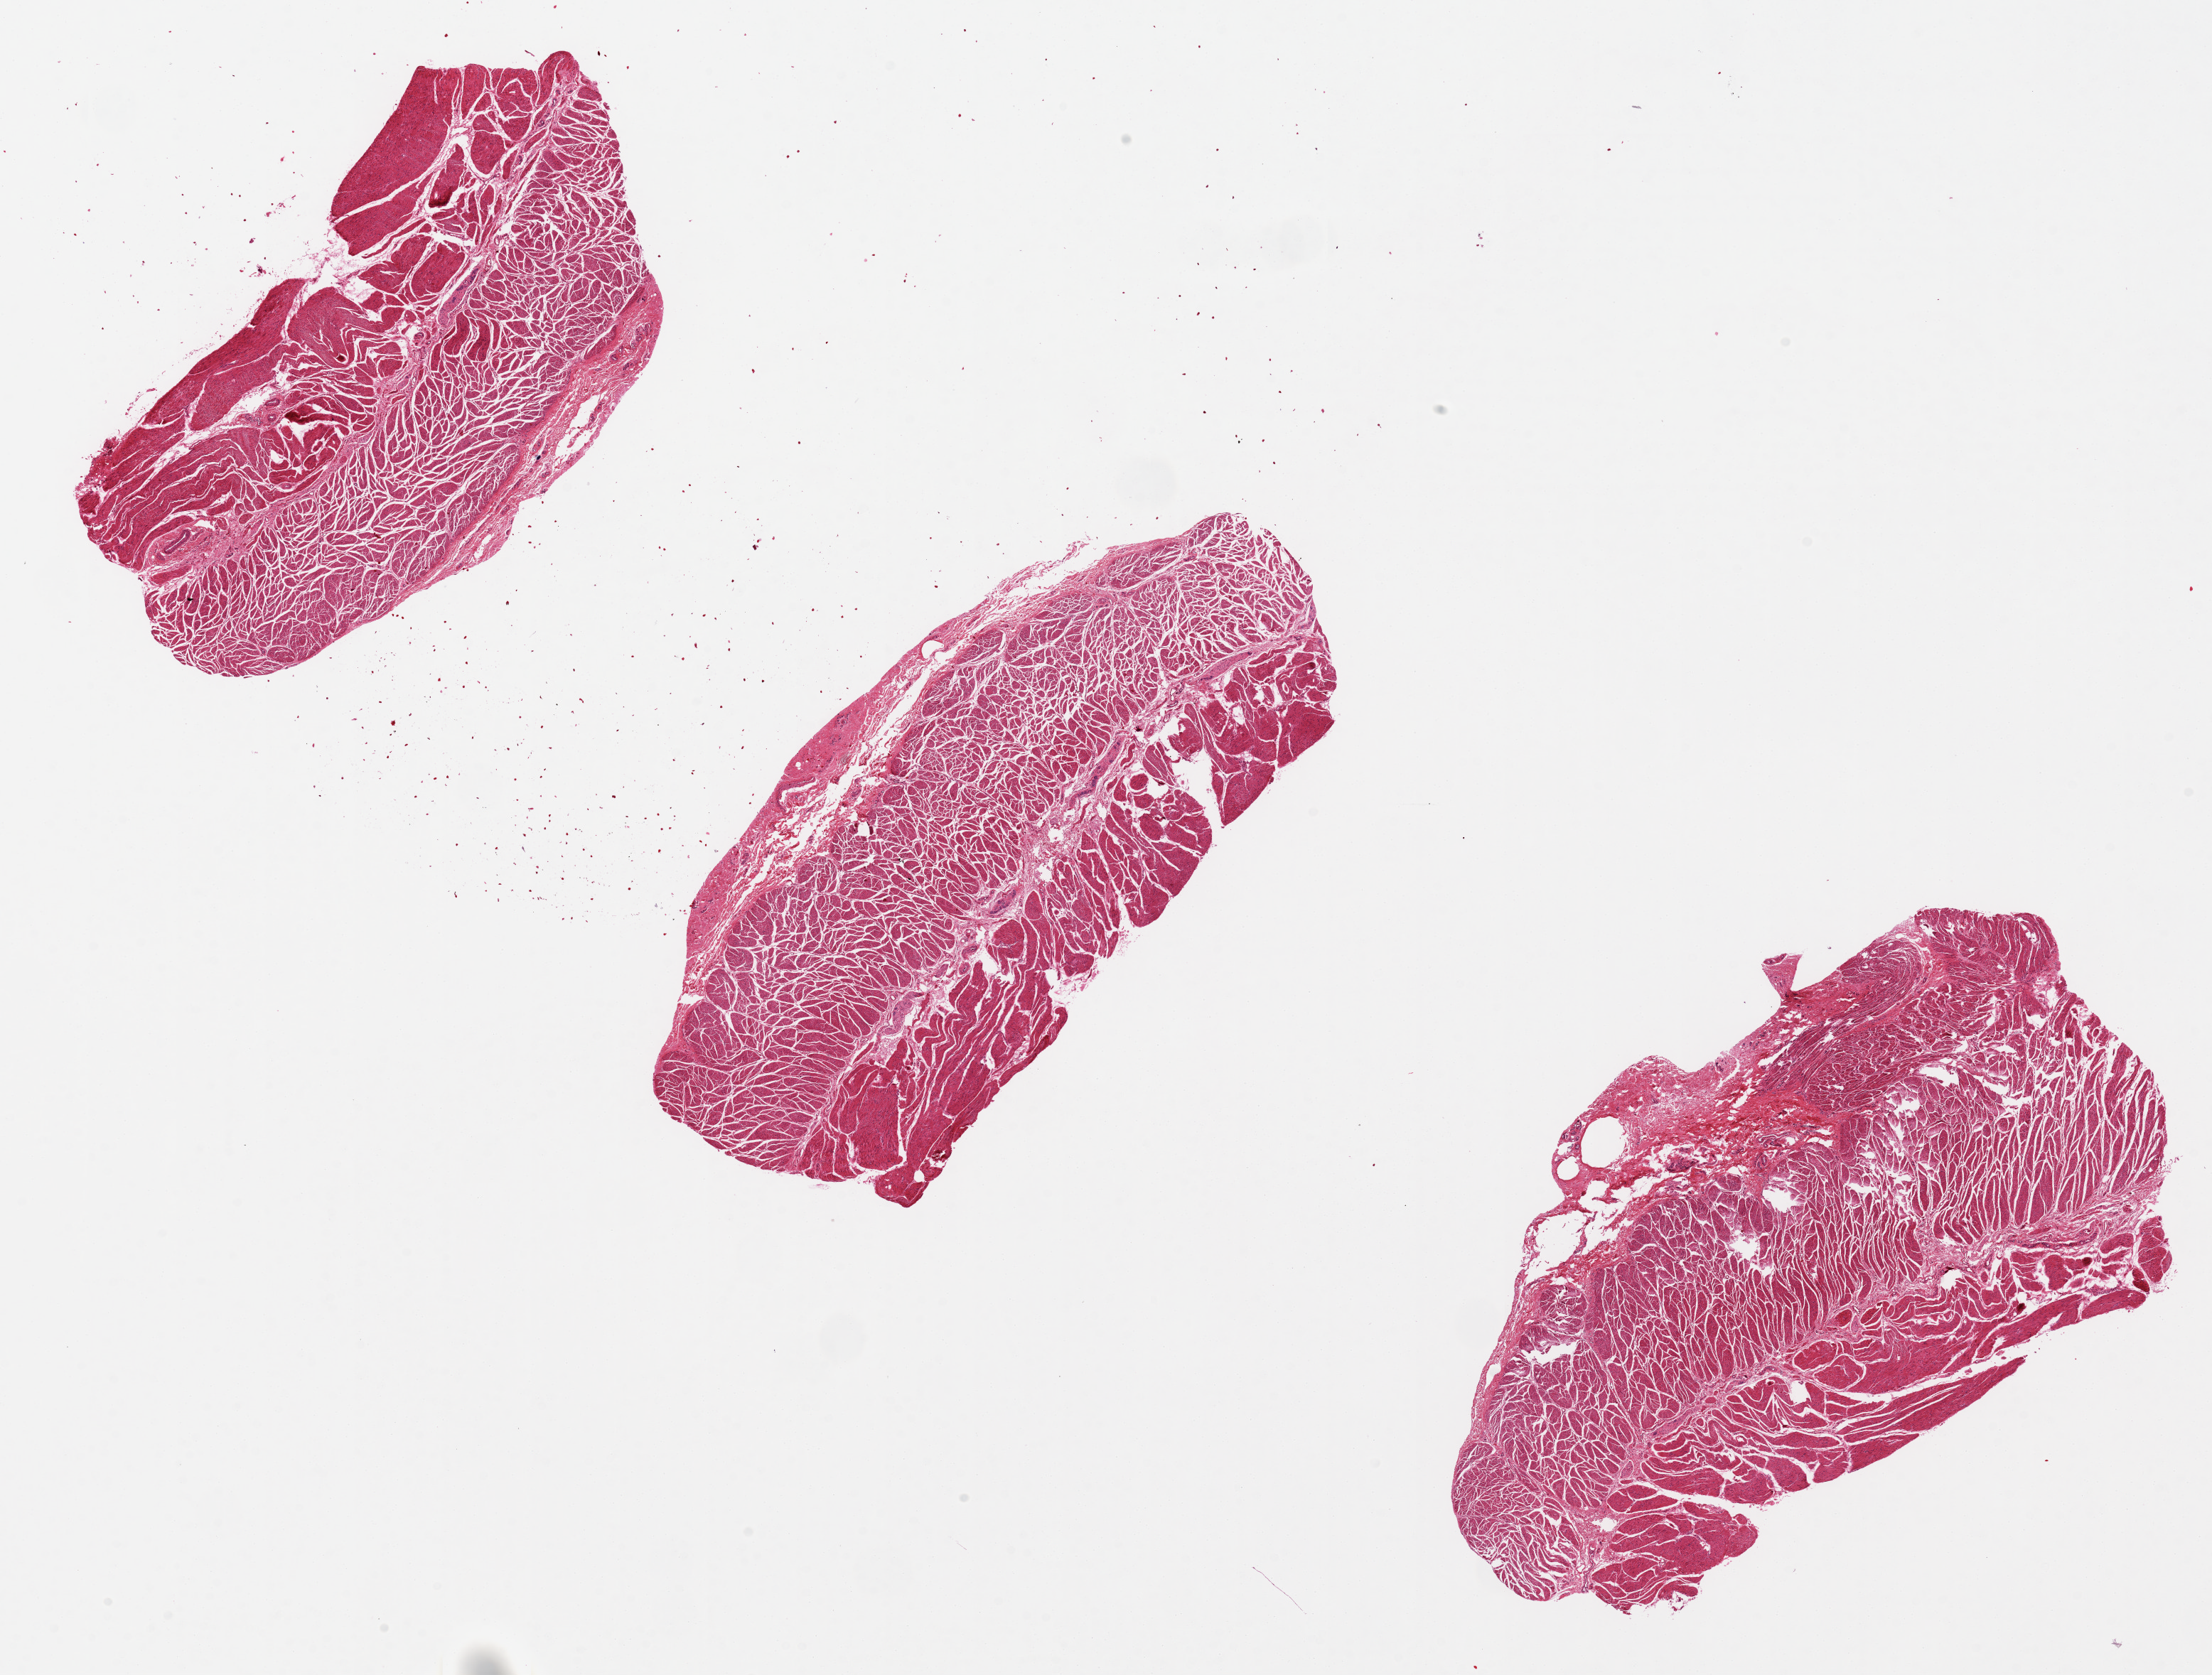
Hematoxylin and eosin (H&E) whole-slide image, brightfield — low-resolution overview of the scanned area, about 24.6 x 18.6 mm; PAXgene-fixed paraffin-embedded (PFPE) section; target tissue: esophageal muscle; tissue donor sample. Male donor.
Review note (as recorded): 4x9mm. Poor fixation, cracks and separation of sections.